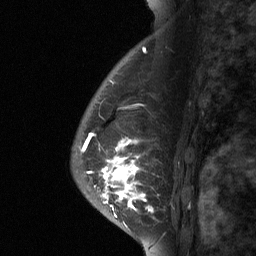
Breast MRI (dynamic contrast-enhanced), one sagittal slice. Slice 49 of 64 in the series (ordered by position). Dynamic contrast-enhanced study with each time point stored as its own series, time point 2 of 3 at this slice position (early post-contrast, ordered by acquisition time). 1.5 T. TE 4.8 ms, TR 27 ms. 2 mm slice thickness. 256 × 256 image matrix, field of view 180 × 180 mm. Patient: female, 56 years. Case-level facts recorded for this patient, not image findings: setting: breast cancer imaged before/during neoadjuvant chemotherapy; receptor status: HER2-positive.
Structures marked on this image (semi-automatic segmentation, software-assisted and operator-edited):
- analysis volume of interest (the breast-tissue region the enhancement analysis was run in; not a lesion): bounding box <96,104,182,229> (left, top, right, bottom; pixels)
- tumour enhancement mask (voxels above the 90 % enhancement threshold inside the analysis volume of interest): <98,137,153,217>